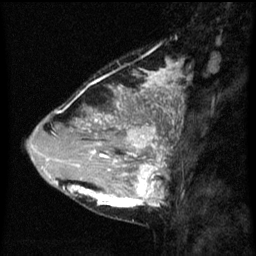
Breast MRI (dynamic contrast-enhanced), one sagittal slice. Slice 21 of 60 in the series (ordered by position). Dynamic contrast-enhanced series, image 2 of 3 at this slice position (ordered by acquisition). 1.5 T. TE 4.2 ms, TR 8 ms. 256 × 256 image matrix. Patient: female, 33 years.
Annotated regions visible in this slice (semi-automatic segmentation, software-assisted and operator-edited):
- analysis volume of interest (the breast-tissue region the enhancement analysis was run in; not a lesion): box from (x=71, y=118) to (x=171, y=209) px
- tumour enhancement mask (voxels above the 70 % enhancement threshold inside the analysis volume of interest): (x=71, y=118)–(x=166, y=207)